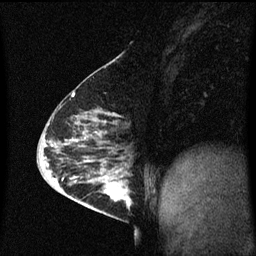
Breast MRI (dynamic contrast-enhanced), one sagittal slice. Position 28 of 60 along the scan axis. Dynamic contrast-enhanced series, image 2 of 3 at this slice position (ordered by acquisition). 1.5 T. TE 4.2 ms, TR 8.4 ms. 2 mm slice thickness. 256 × 256 image matrix. Patient: female, 63 years.
Structures marked on this image (semi-automatically segmented with operator editing):
- analysis volume of interest (the breast-tissue region the enhancement analysis was run in; not a lesion): box from (x=98, y=168) to (x=135, y=217) px
- tumour enhancement mask (voxels above the 70 % enhancement threshold inside the analysis volume of interest): (x=98, y=168)–(x=131, y=209)